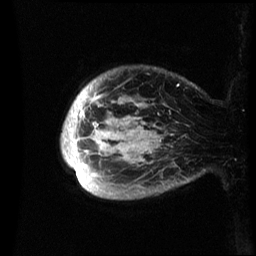
Breast MRI (dynamic contrast-enhanced), one sagittal slice. Position 4 of 60 along the scan axis. Dynamic contrast-enhanced series, image 2 of 3 at this slice position (ordered by acquisition). 1.5 T. TE 4.2 ms, TR 8.4 ms. 256 × 256 image matrix. Female patient, age 48 years.
Outlined on this slice (semi-automatically segmented with operator editing):
- analysis volume of interest (the breast-tissue region the enhancement analysis was run in; not a lesion): bounding box [x1, y1, x2, y2] px = [61, 70, 194, 199]
- tumour enhancement mask (voxels above the 70 % enhancement threshold inside the analysis volume of interest): [62, 84, 179, 182]